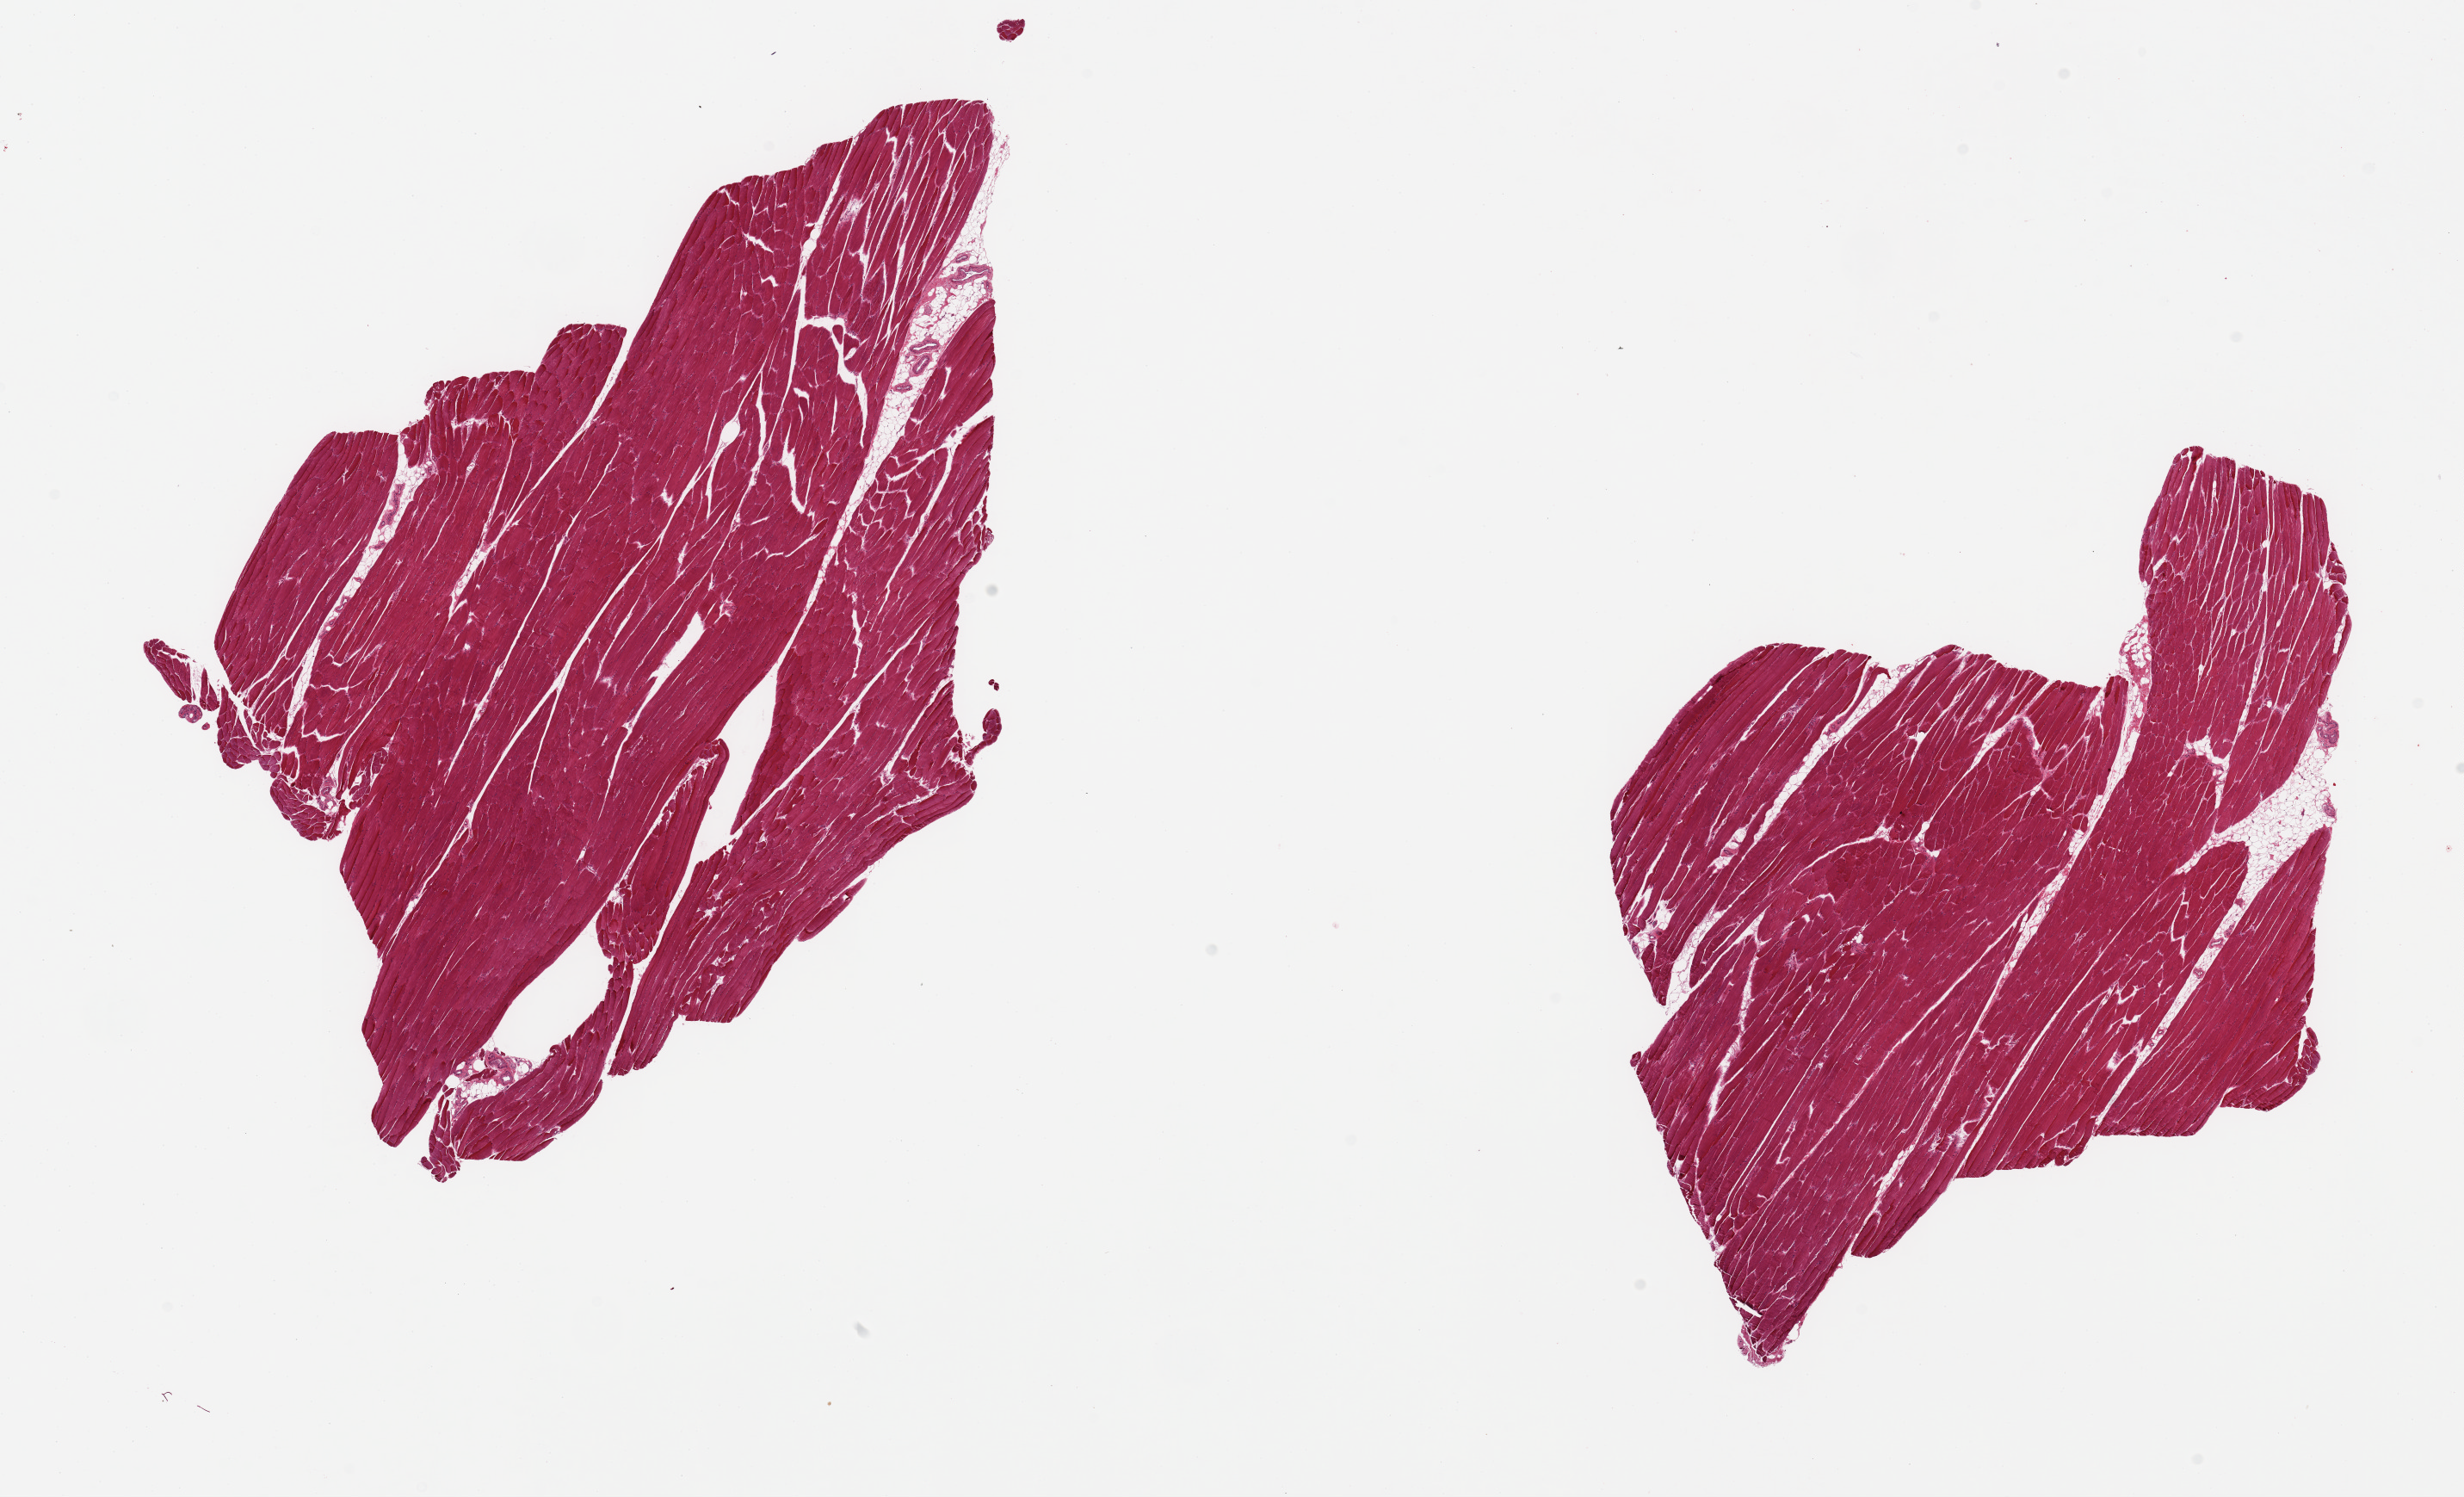
H&E whole-slide image, a low-resolution overview of the entire scanned area, about 22.6 x 13.8 mm. PAXgene-fixed paraffin-embedded (PFPE) section. Sampled site (target tissue): skeletal muscle. Donor tissue sample. Donor sex: male.
Reviewer comment on this tissue sample: 2 pieces; well trimmed; 5% internal fat.